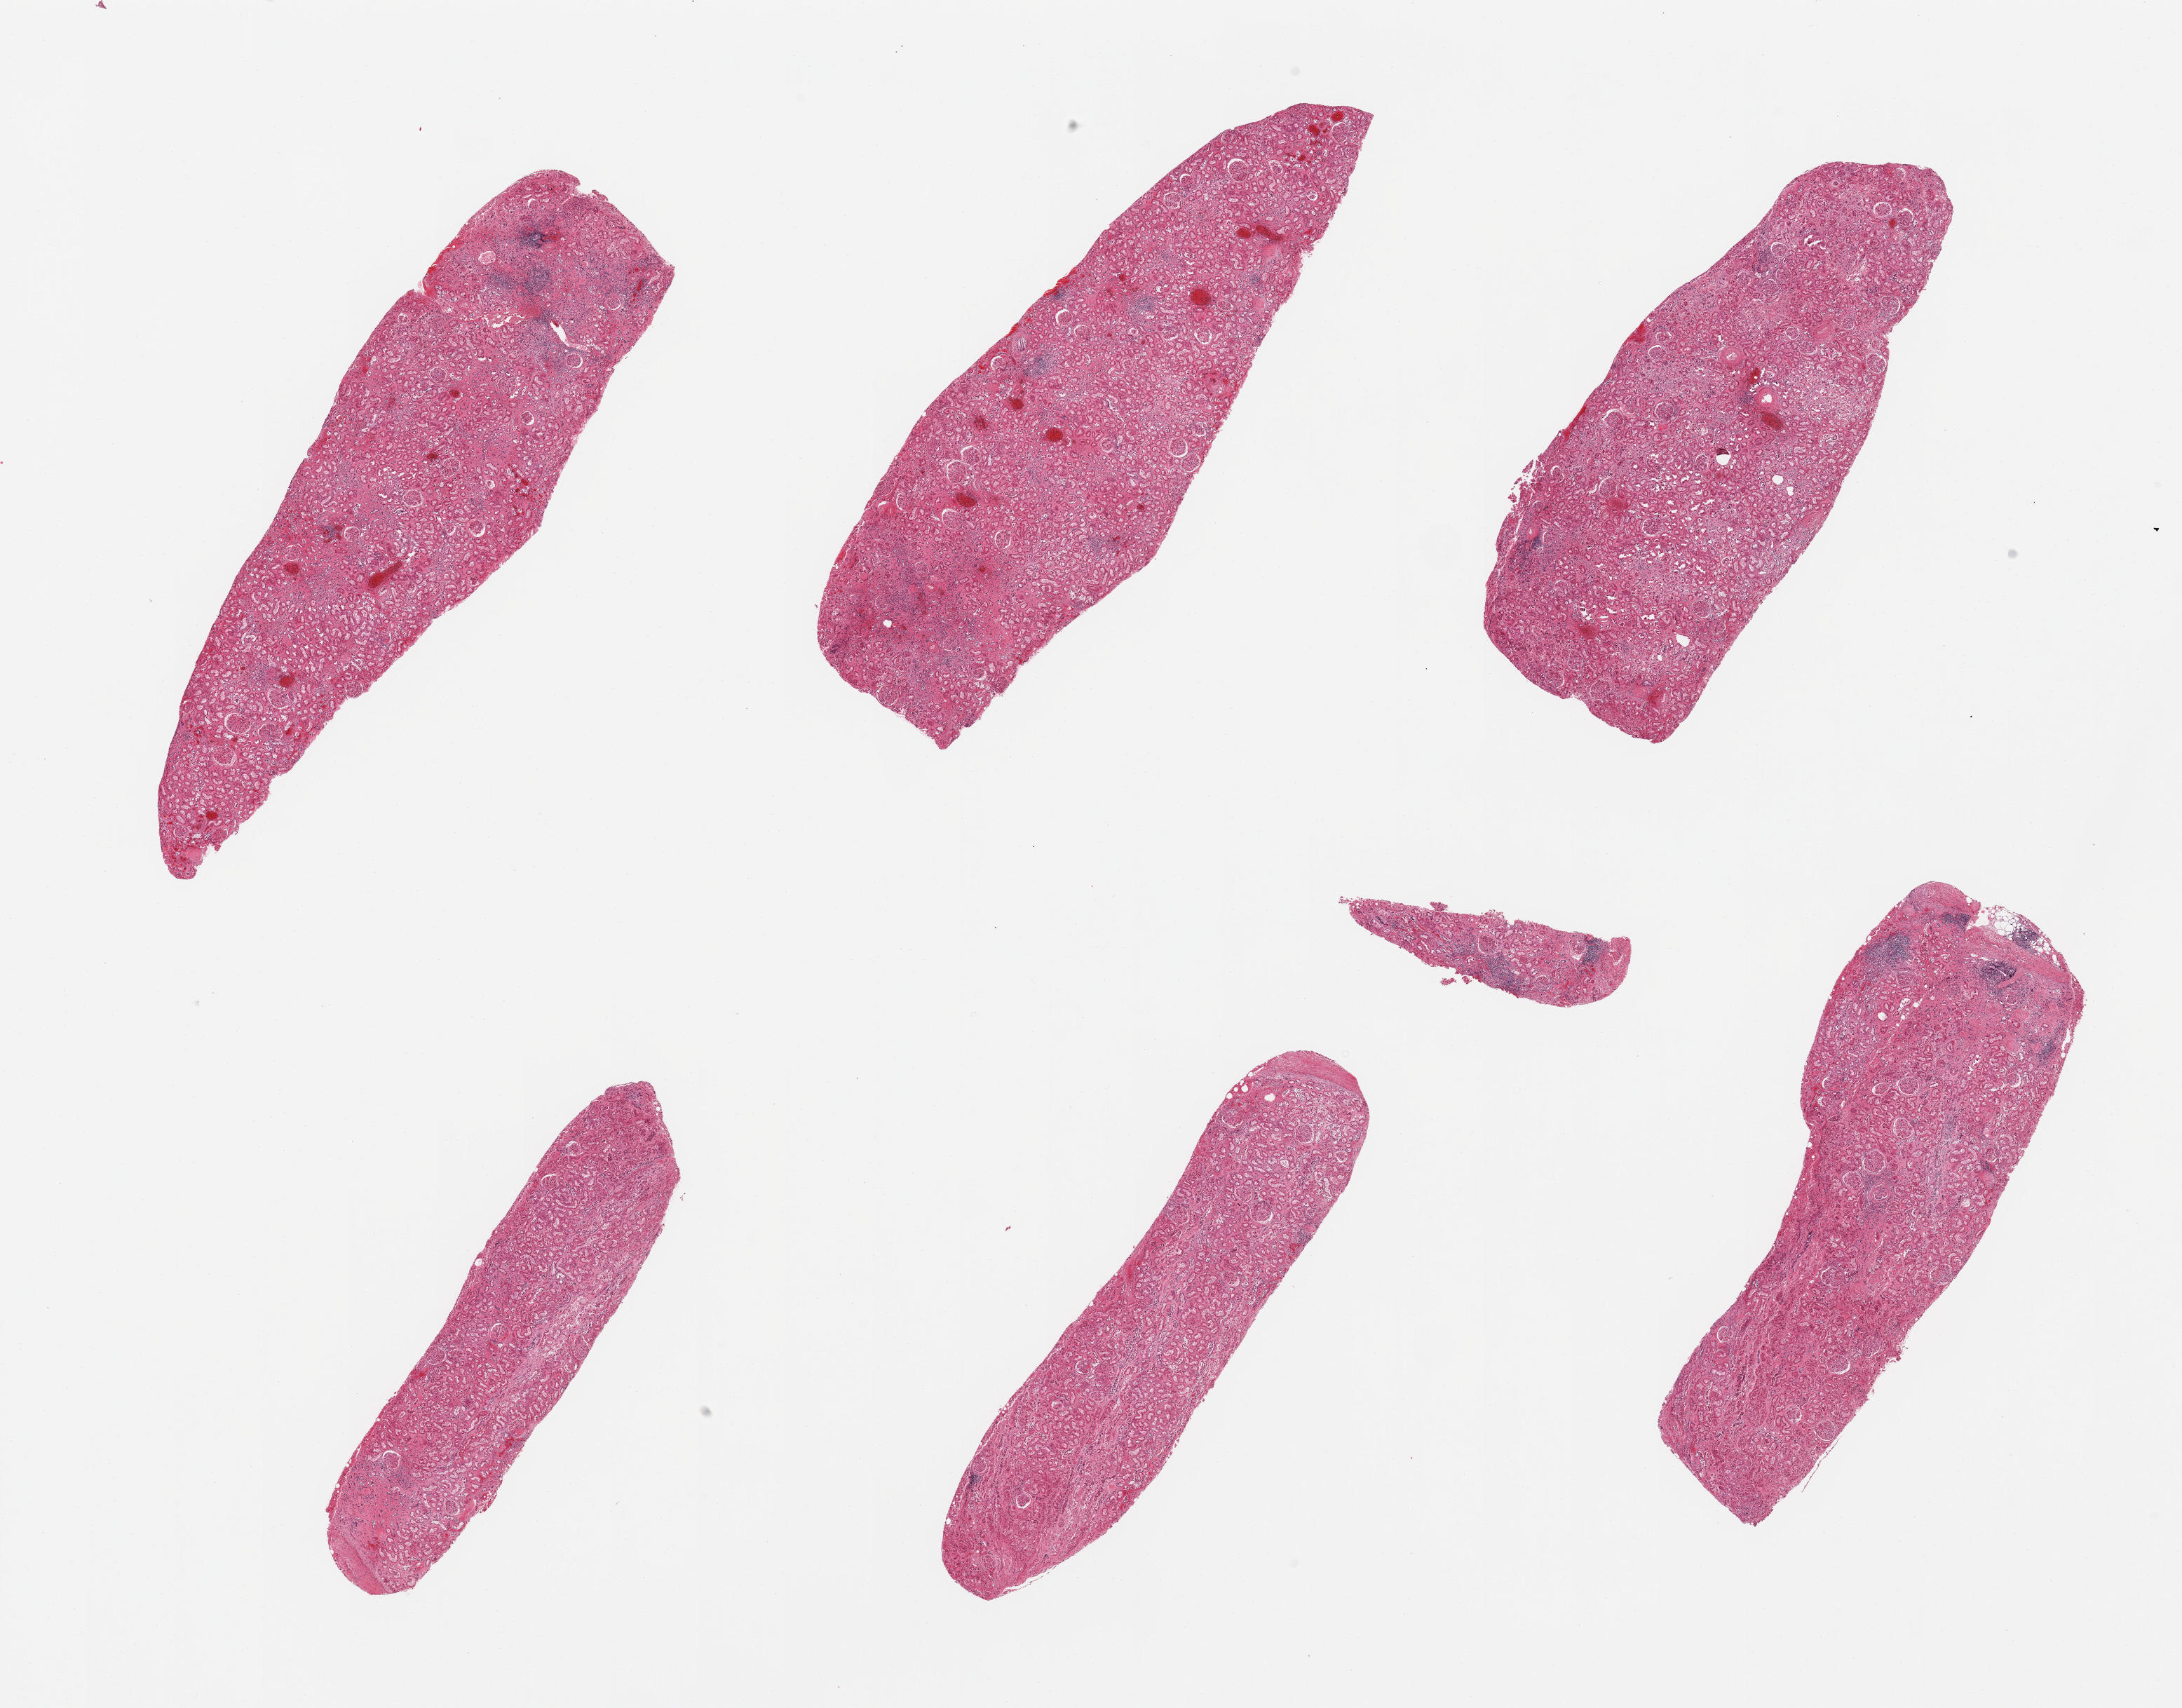
Hematoxylin and eosin (H&E) whole-slide image, low-resolution overview of the scanned area, about 24.6 x 19.3 mm. PAXgene-fixed, paraffin-embedded tissue. Section of renal cortex (target tissue). Donor tissue sample. Male donor.
Review note (as recorded): 6 pieces, glomeruli present, patchy interstitial chronic nephritis, tubules with advanced autolysis.